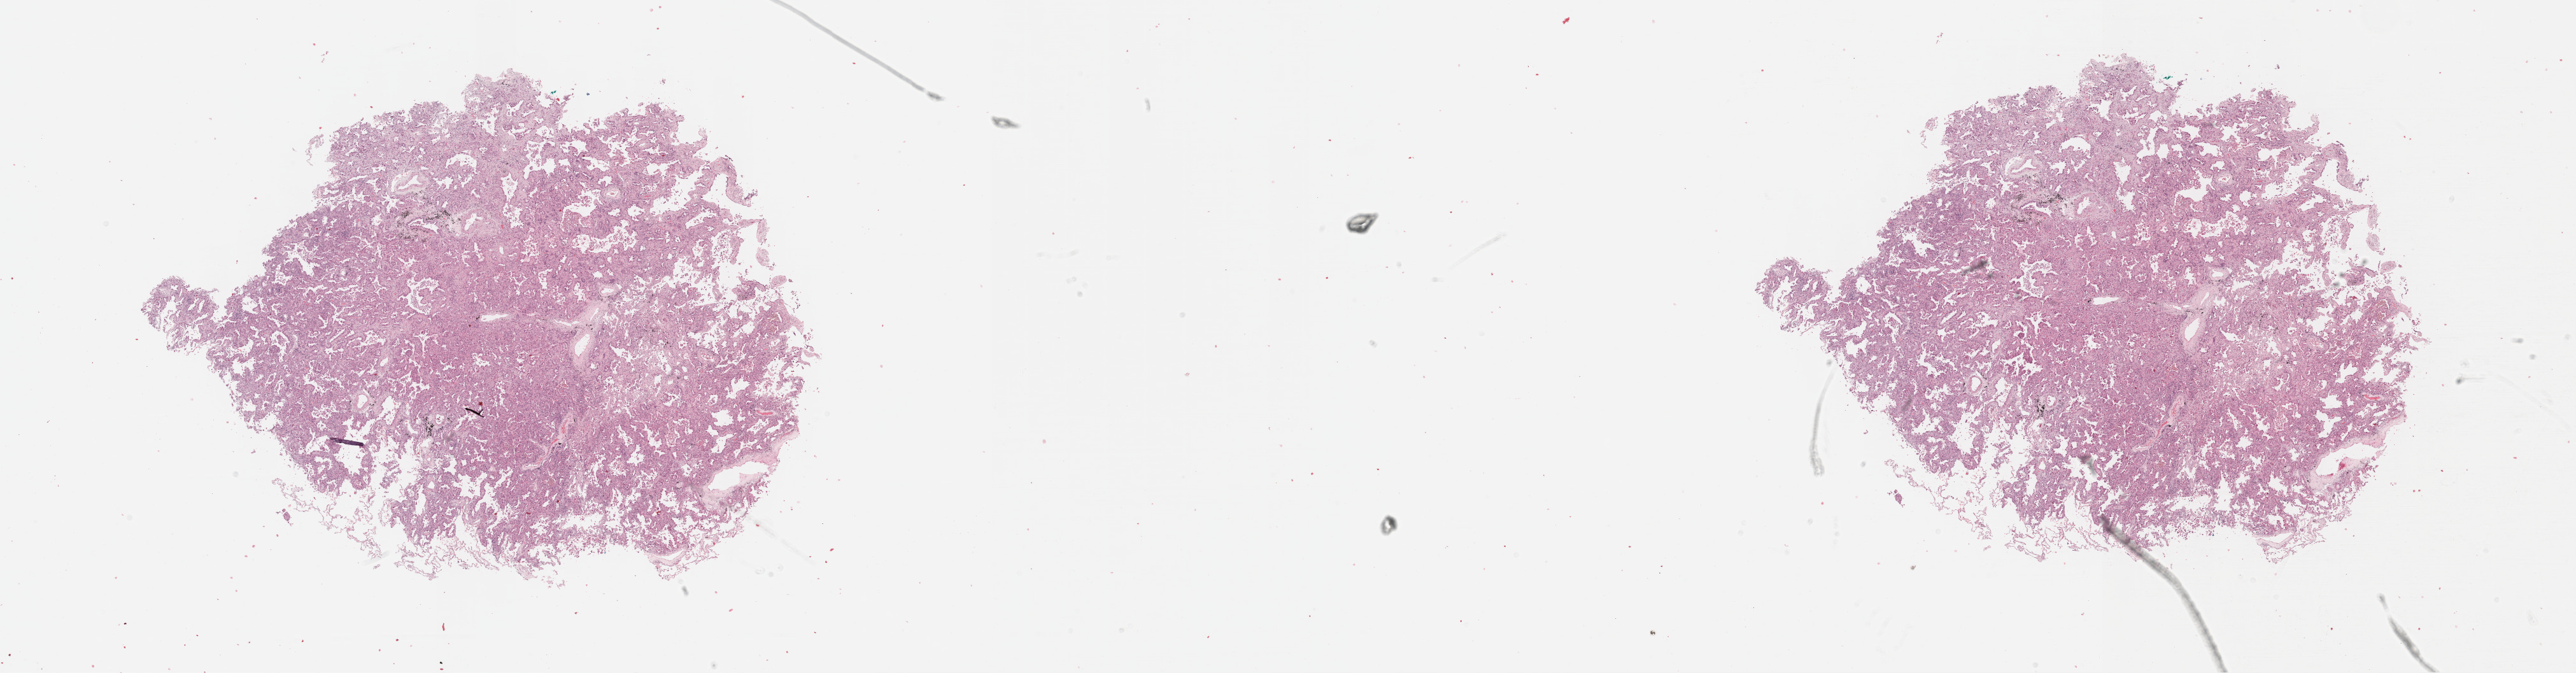
Hematoxylin and eosin (H&E) stained whole-slide image — shown as a low-resolution overview of the whole scanned area (about 32.7 x 8.5 mm, from a 40x scan), formalin-fixed paraffin-embedded (FFPE) diagnostic section, sample: primary tumour, lung. Patient: female, age at initial diagnosis 70 years.
Pathologic diagnosis: Adenocarcinoma, NOS (upper lobe, lung). AJCC pathologic stage: IA. TNM: T1 N0 M0.